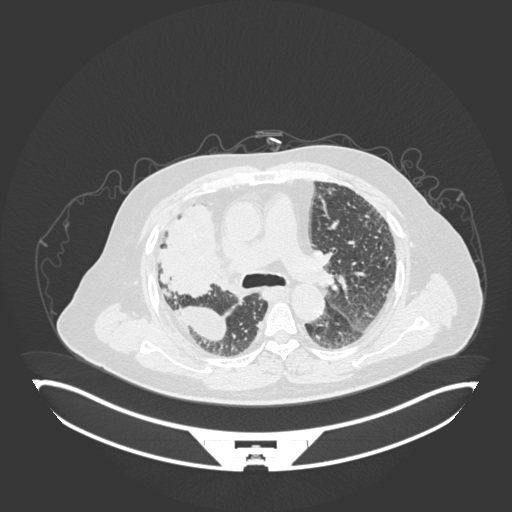
Chest CT, one axial slice. Position 110 of 201 along the scan axis. 120 kVp. Lung window (W 1500 / L -600 HU). 1 mm slice thickness. 512 × 512 image matrix, field of view 500 × 500 mm. Male patient, age 69 years. Case-level facts recorded for this patient, not image findings: clinical TNM (as recorded): T4 N3 M1.
Annotated regions visible in this slice (bounding box drawn by a radiologist):
- lung tumour (recorded histology: adenocarcinoma): box from (x=160, y=203) to (x=232, y=305) px